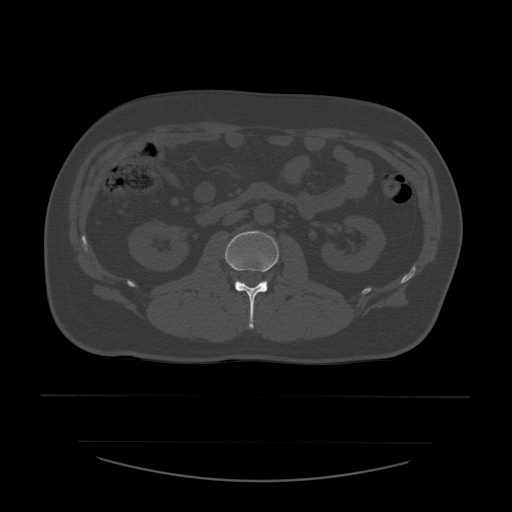
CT including the spine, one axial slice; position 196 of 532 along the scan axis; reconstruction kernel STANDARD; 120 kVp; bone window (W 1800 / L 400 HU); 1.25 mm slice thickness; 512 × 512 image matrix, field of view 441 × 441 mm. Patient age 44 years. Case-level facts recorded for this patient, not image findings: primary cancer: soft tissue sarcoma.
Annotated regions visible in this slice (semi-automatic segmentation, software-assisted and operator-edited):
- L2 vertebra: box from (x=225, y=231) to (x=279, y=329) px